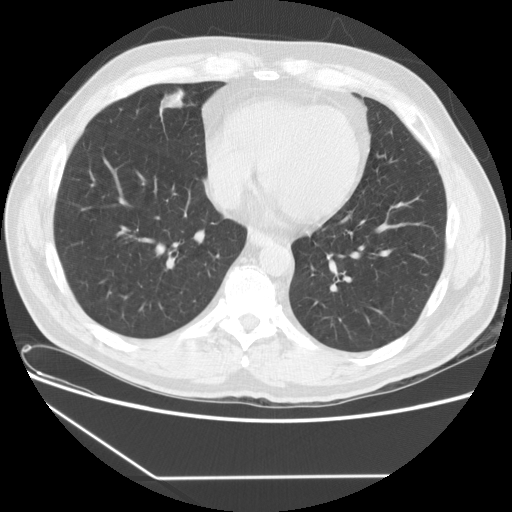
Chest CT (low-dose screening protocol), one axial image; baseline screening round; lung window (W 1500 / L -600 HU); standard (soft-tissue) reconstruction kernel (STANDARD); 120 kVp; slice 103 of 154 in the series; 512 × 512 image matrix. Male, age 59 years at enrolment. Current smoker at enrolment.
Expert reader's lesion annotation, box from (x=153, y=87) to (x=197, y=117) px. No non-calcified nodule or mass ≥4 mm was recorded by the screening reader at this exam. Participant outcome: lung cancer diagnosed 58 days after this screen — oat cell carcinoma, right middle lobe, stage IIA (AJCC 6th edition), 15 mm at pathology.